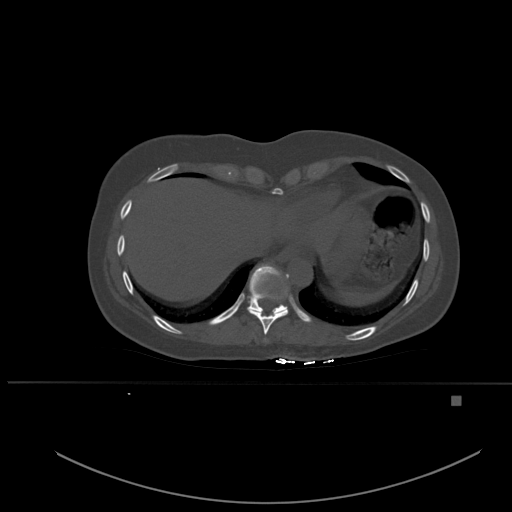
CT including the spine, one axial slice. Slice 299 of 651 in the series (ordered by position). Bone window (W 1800 / L 400 HU). 1.5 mm slice thickness. 512 × 512 image matrix, field of view 443 × 443 mm. Patient: female, 49 years. Case-level facts recorded for this patient, not image findings: primary cancer: breast.
Annotated regions visible in this slice (semi-automatic segmentation, software-assisted and operator-edited):
- T10 vertebra: box from (x=248, y=264) to (x=287, y=313) px
- T8 vertebra: (x=264, y=339)–(x=266, y=342)
- T9 vertebra: (x=247, y=274)–(x=289, y=335)